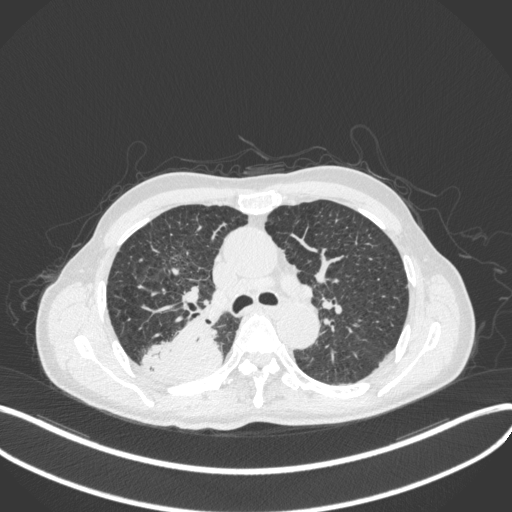
Chest CT, one axial slice. Slice 299 of 423 in the series (ordered by position). Reconstruction kernel B31f. 120 kVp. Lung window (W 1500 / L -600 HU). 1 mm slice thickness. 512 × 512 image matrix, field of view 400 × 400 mm. Patient: male, 79 years. From the clinical record (not read from this slice): clinical TNM (as recorded): T3 N0 M0.
Structures marked on this image (rectangle marked by the reading radiologist):
- lung tumour (recorded histology: adenocarcinoma): bounding box (x1, y1, x2, y2) in pixels: (137, 314, 224, 386)